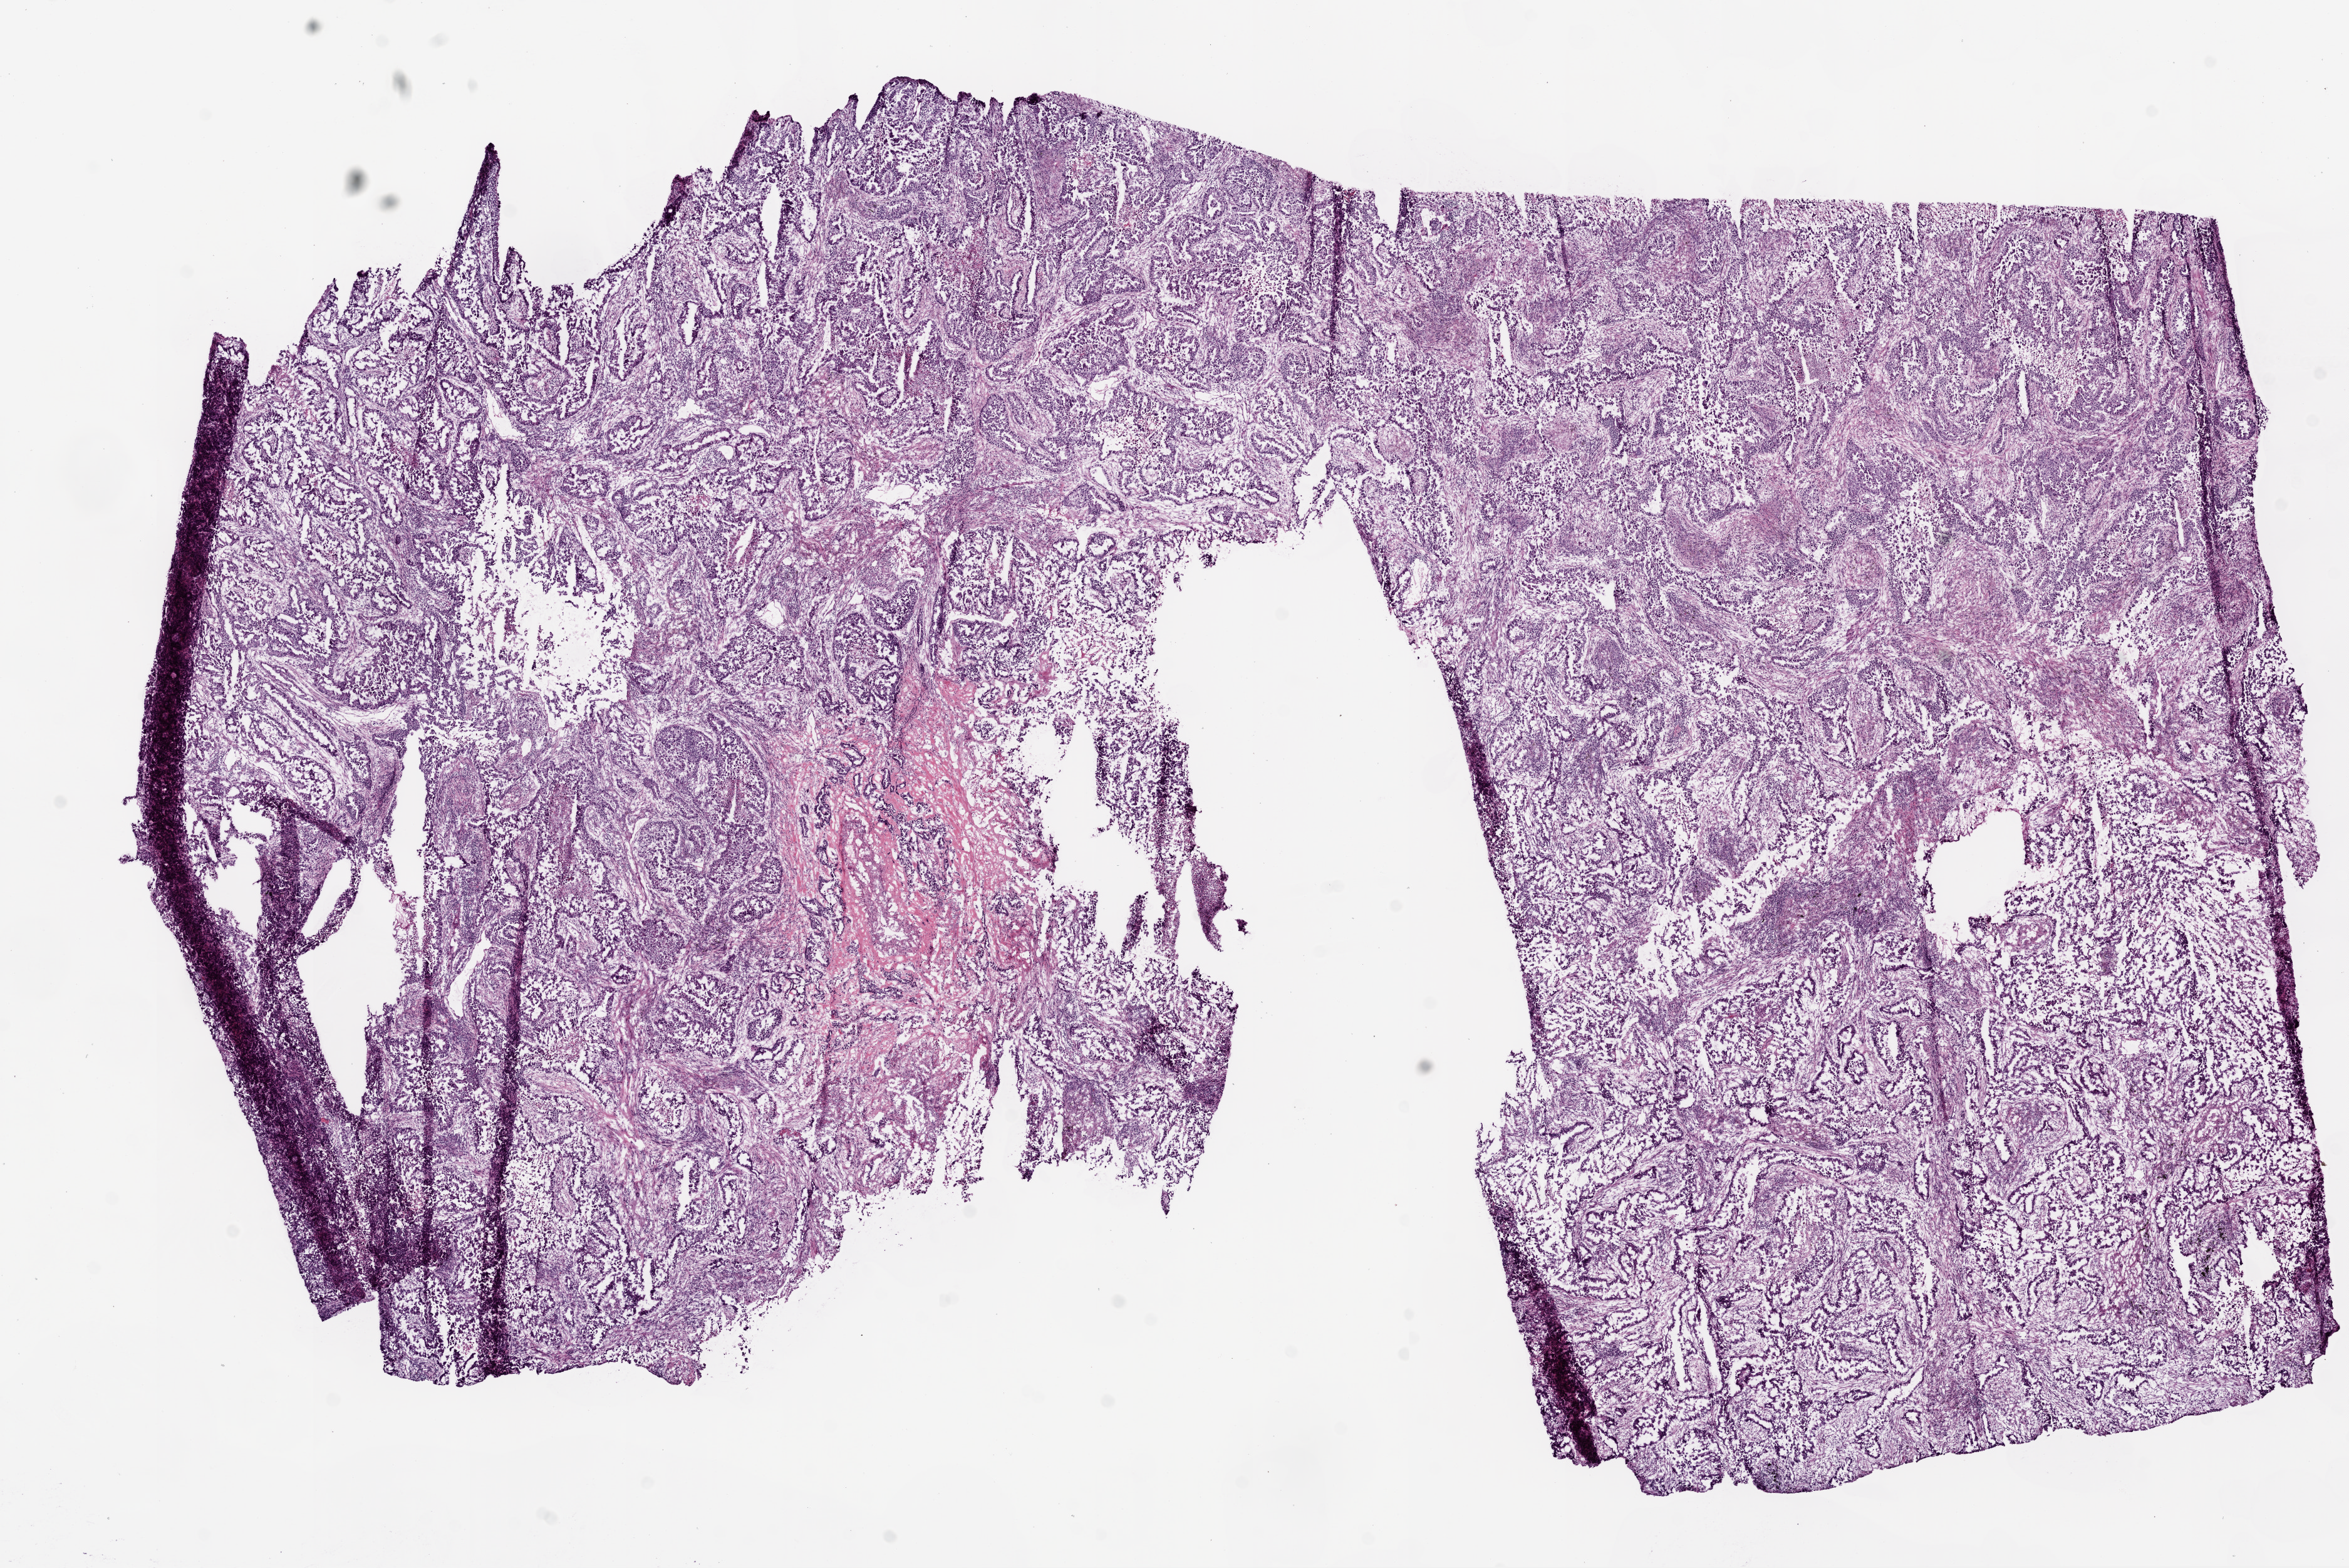
Digitized Hematoxylin and eosin (H&E) stained tissue section (whole slide) — low-resolution overview of the scanned area, about 15.0 x 10.0 mm (acquisition: 20x scan). Frozen section from the top of the tissue portion. Primary tumour sample from the lung. Female, age 58 years at initial diagnosis. Composition of this section per pathologist review: tumour cells 70%, tumour nuclei 70%, normal cells 0%, stromal cells 25%, necrosis 5%. Infiltration values recorded for this section: lymphocyte infiltration 12%.
* TNM: T2 N0 M0
* diagnosis: Adenocarcinoma with mixed subtypes (upper lobe, lung)
* AJCC pathologic stage: IB (5th edition)